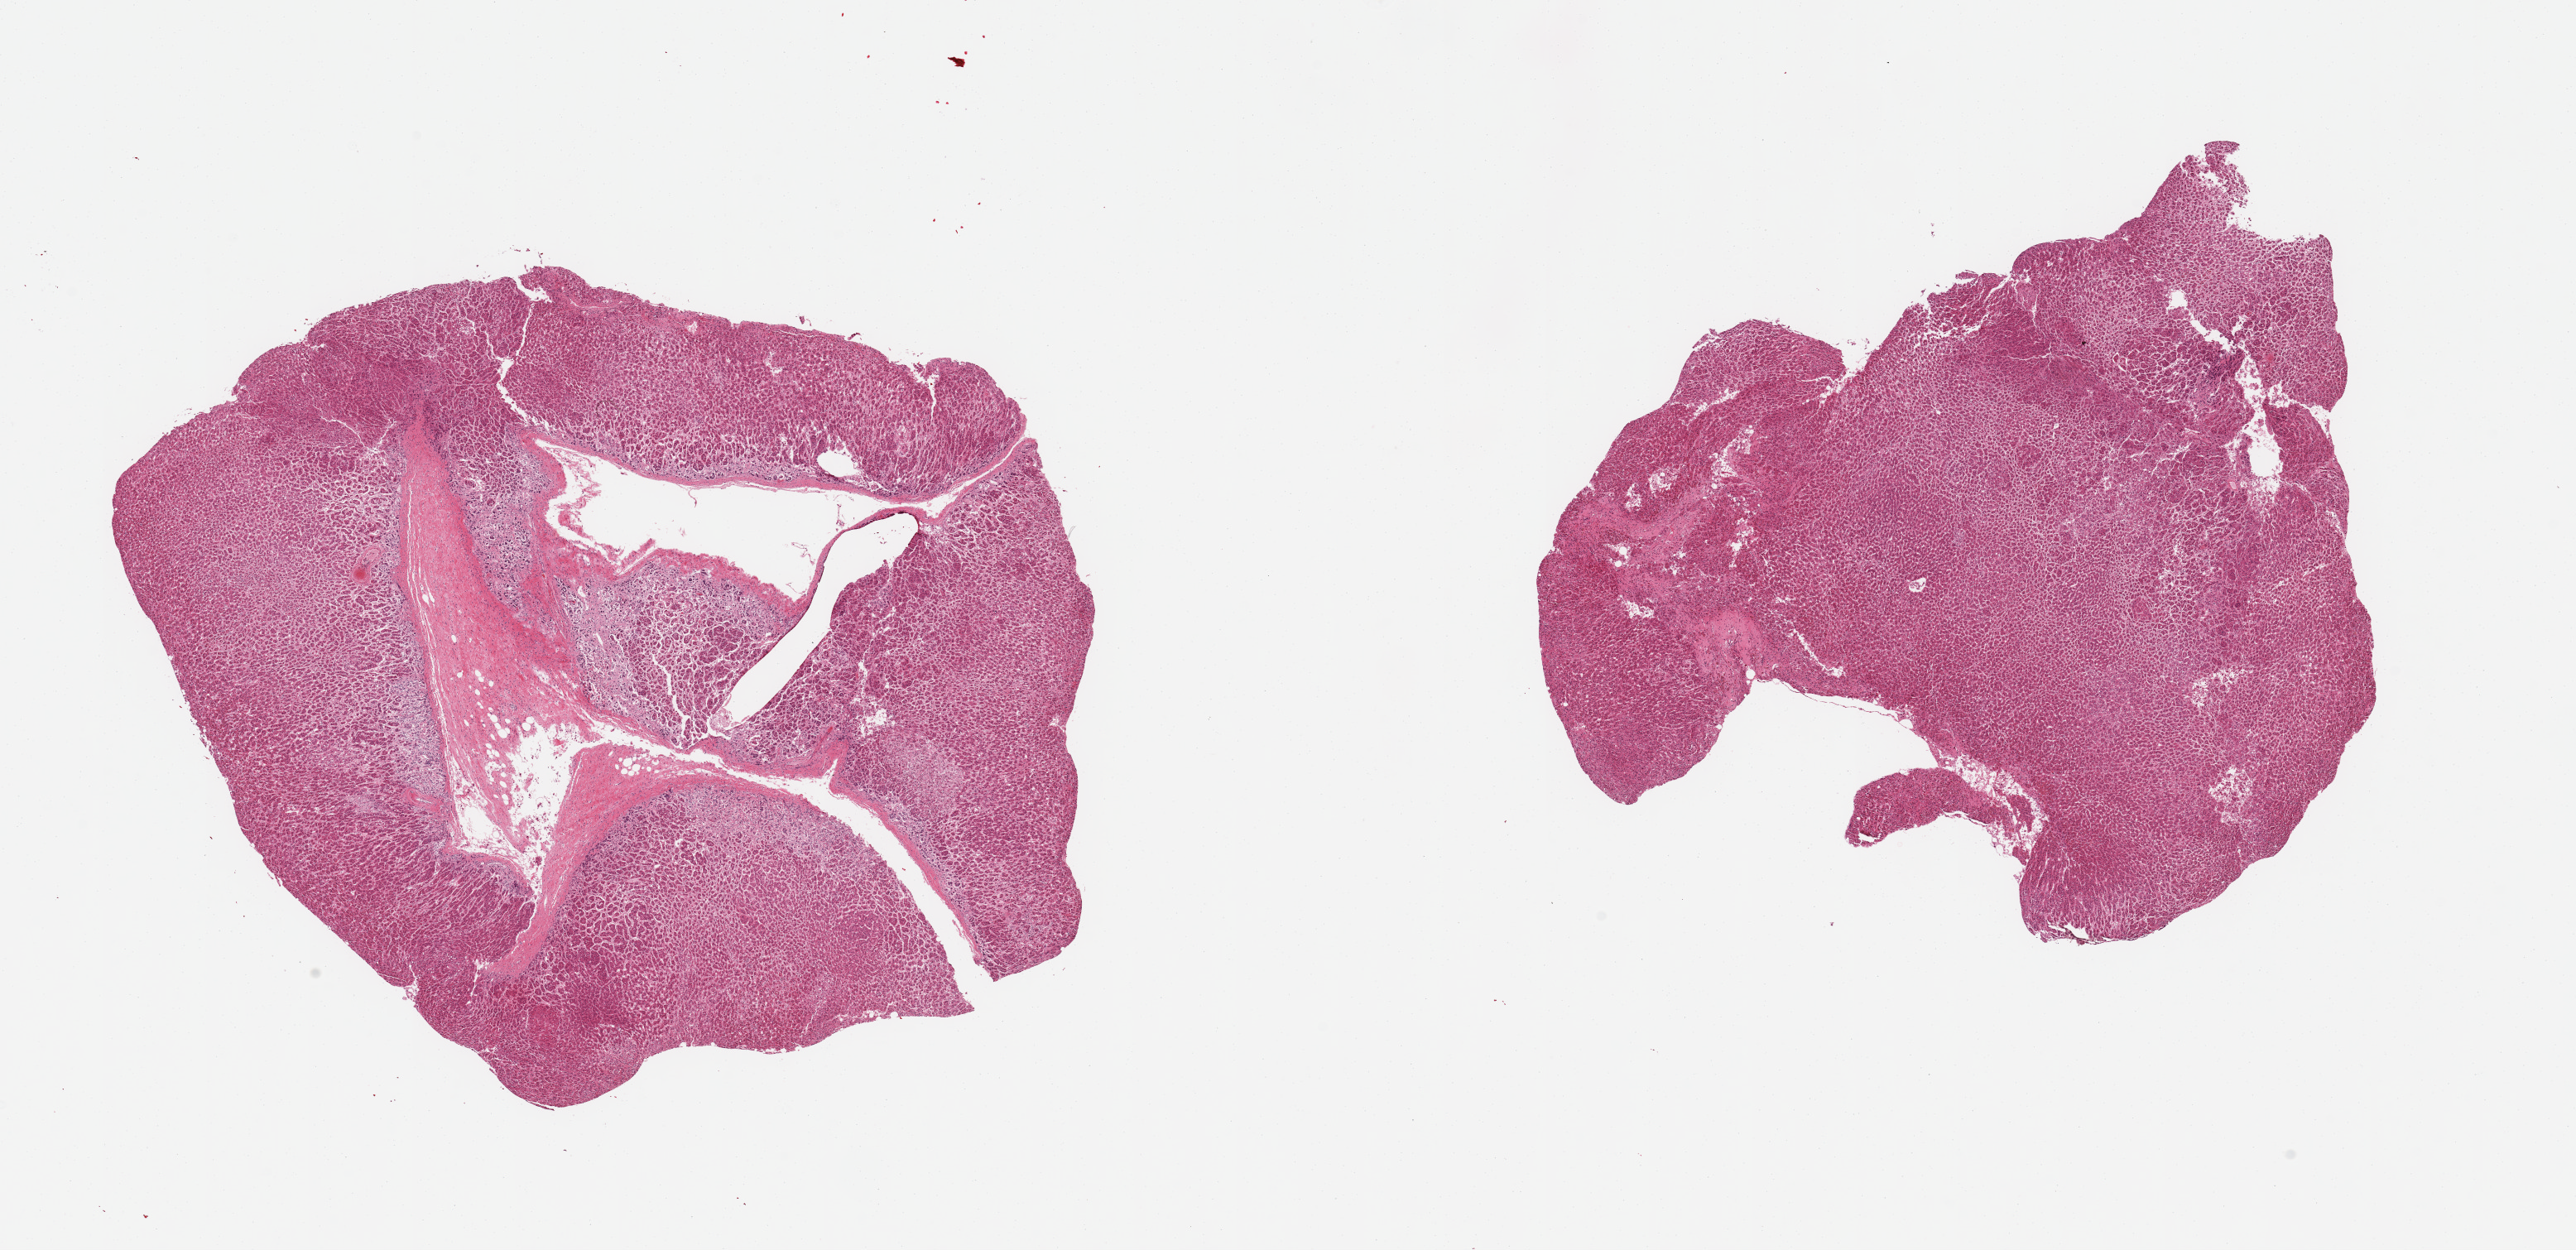
Hematoxylin and eosin (H&E) whole-slide image, shown as a low-resolution overview of the whole scanned area (about 24.6 x 11.9 mm). PAXgene-fixed paraffin-embedded (PFPE) section. Target tissue: adrenal gland. Tissue donor sample. Donor: male.
Reviewer comment on this tissue sample: 2 pieces, cortex, moderately advanced autolysis.